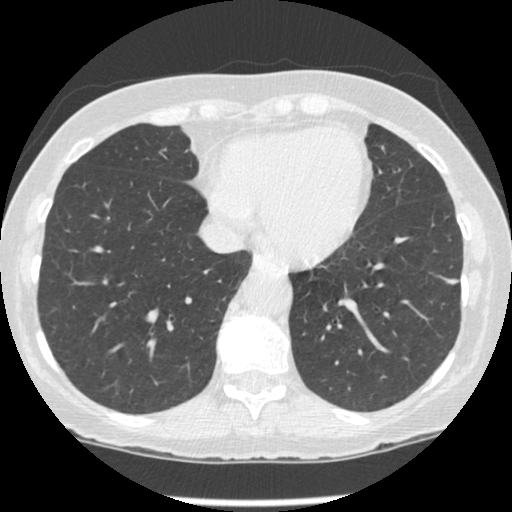
Low-dose screening chest CT, one axial slice. Slice 76 of 247 in the series (ordered by position). Reconstruction kernel STANDARD. Lung window (W 1500 / L -600 HU). 512 × 512 image matrix.
Annotated regions visible in this slice (manually delineated by an expert):
- lesion 1 (tumor, lower lobe of left lung): bounding box [x1, y1, x2, y2] px = [446, 279, 458, 284]